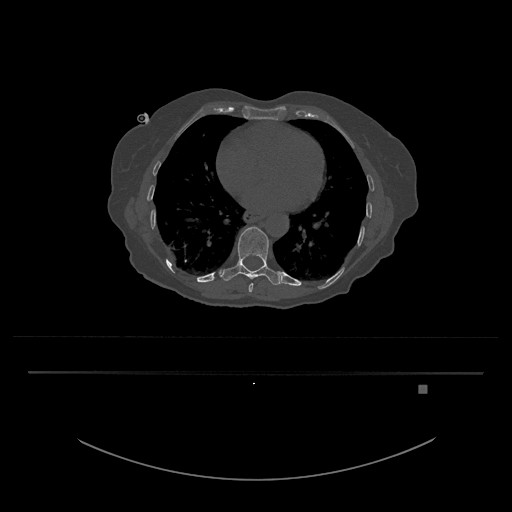
CT including the spine, one axial slice. Position 721 of 797 along the scan axis. Reconstruction kernel Br40s/3. Bone window (W 1800 / L 400 HU). 0.5 mm slice thickness. 512 × 512 image matrix. Patient: female, 57 years. Case-level facts recorded for this patient, not image findings: primary cancer: cervical.
Annotated regions visible in this slice (semi-automatic segmentation, software-assisted and operator-edited):
- T10 vertebra: box from (x=221, y=226) to (x=285, y=285) px
- T9 vertebra: (x=248, y=283)–(x=253, y=293)